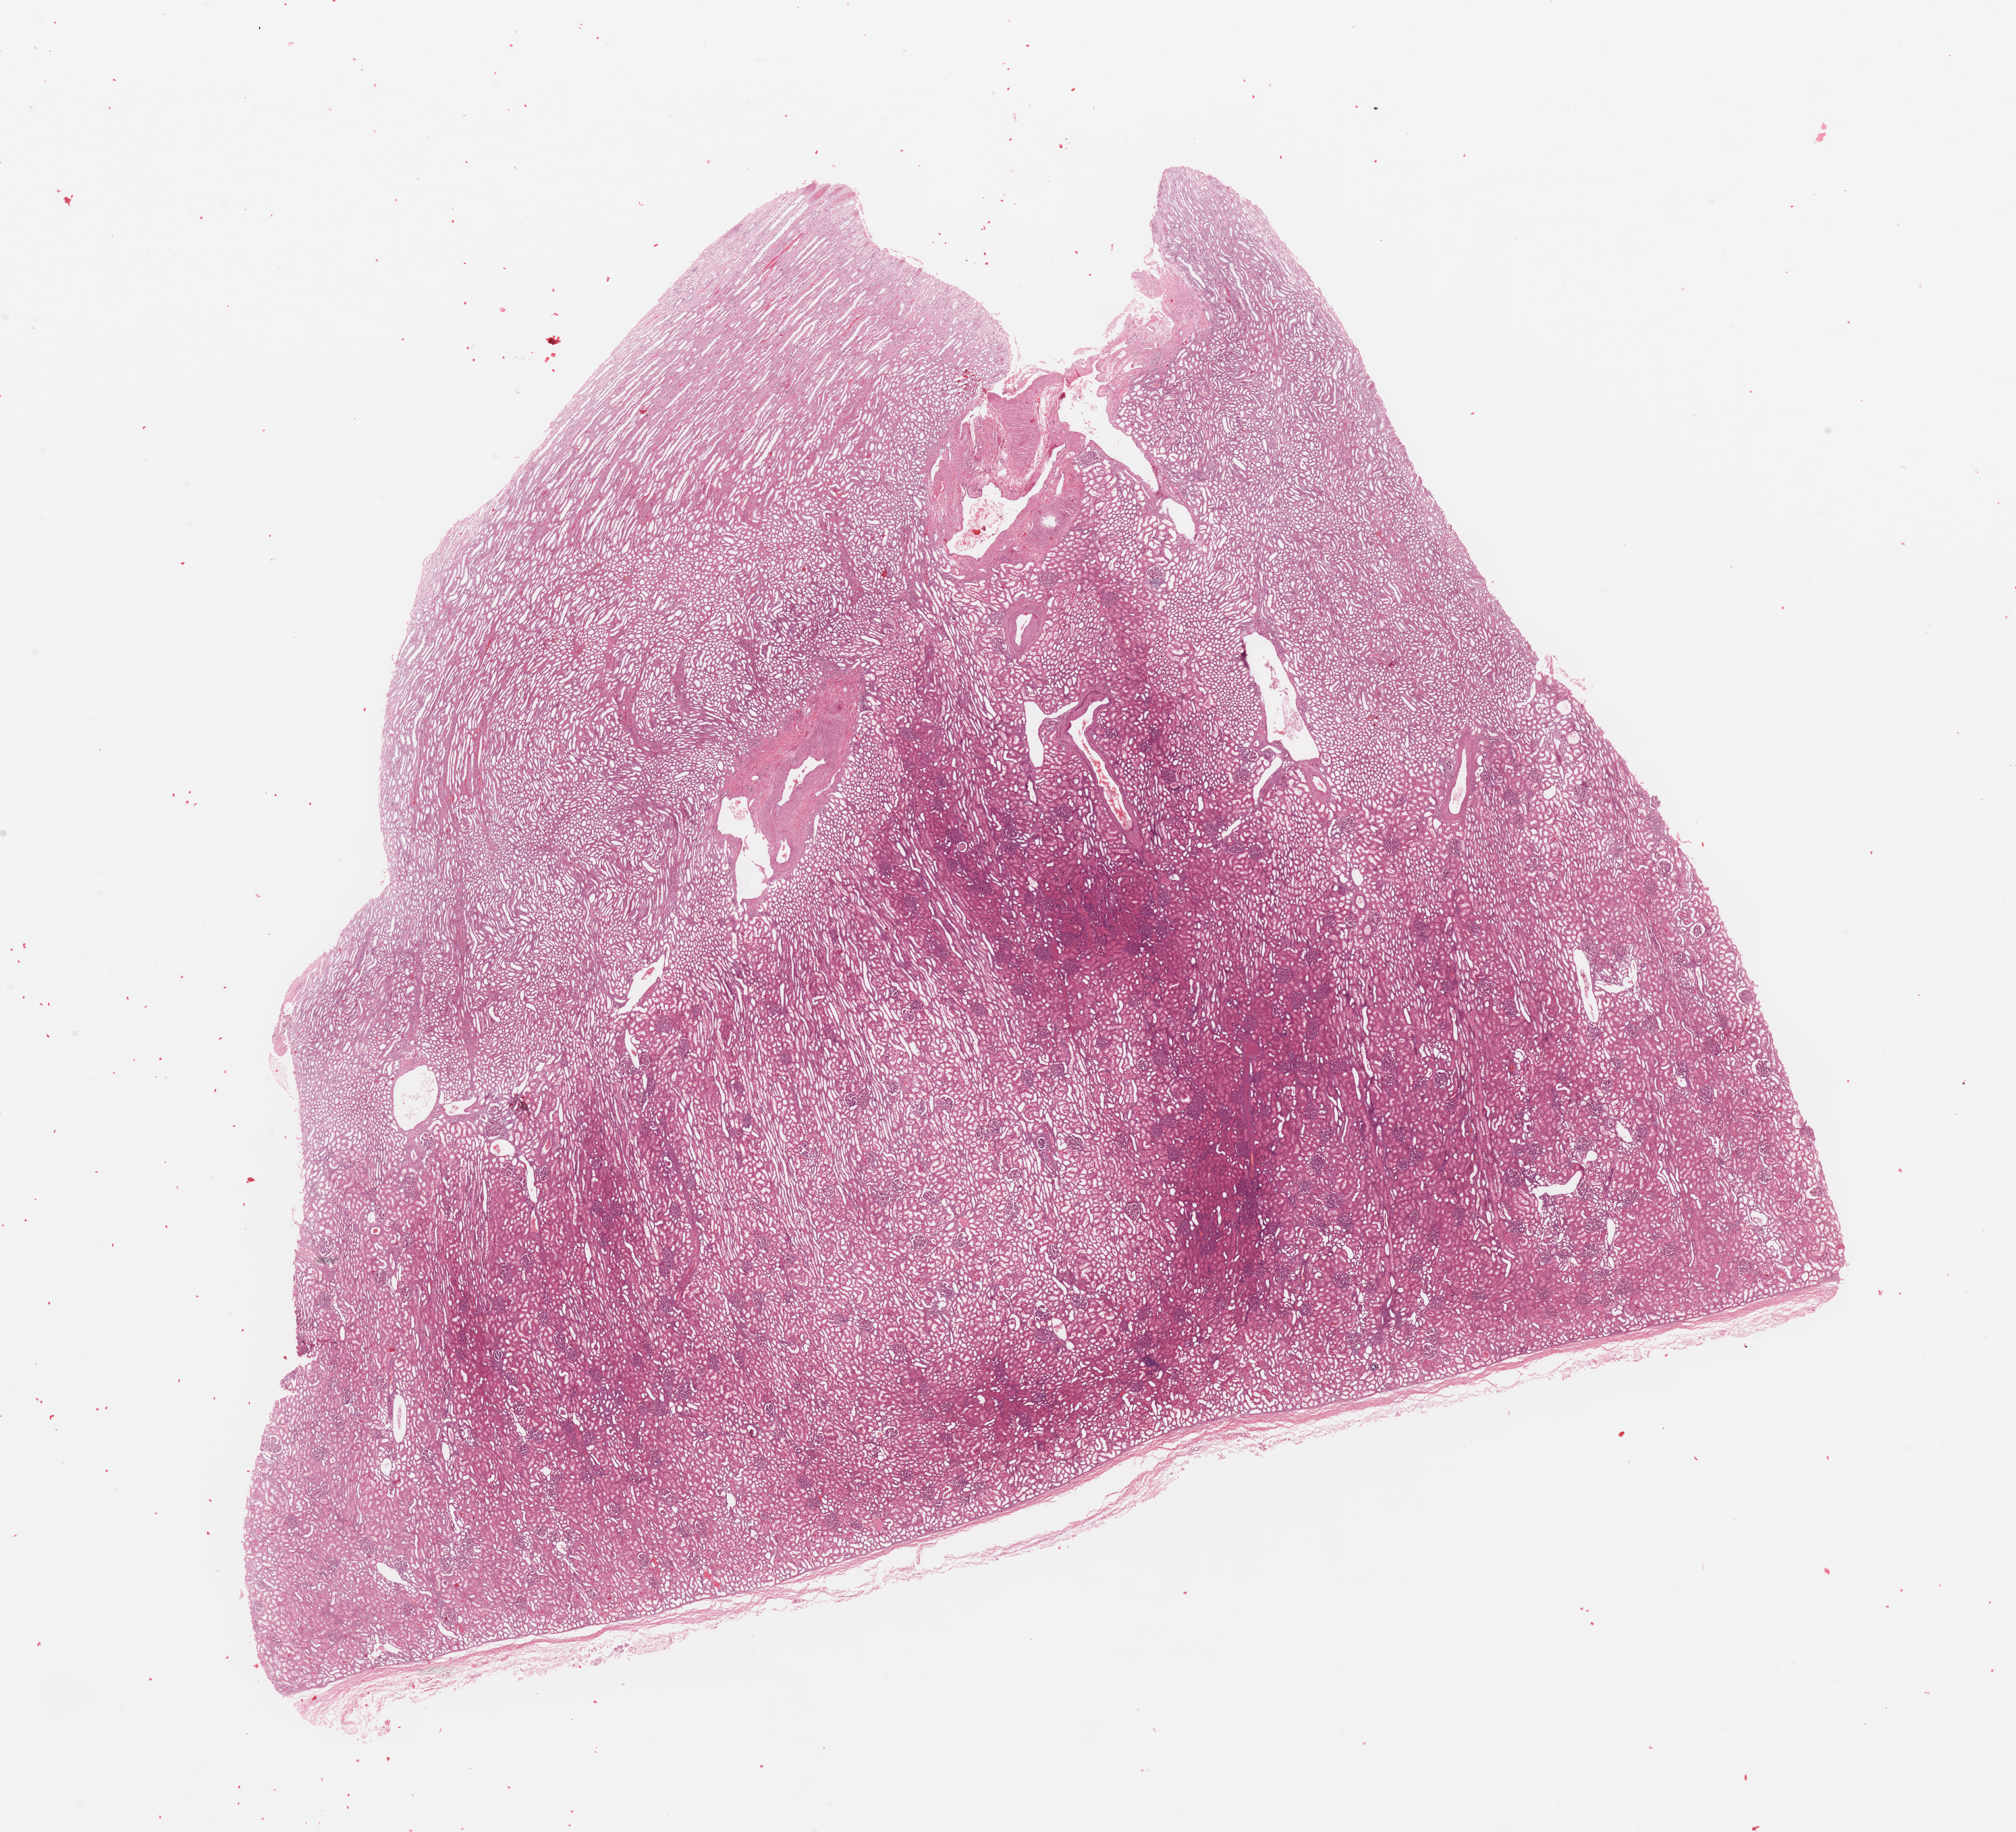
H&E-stained whole-slide image — whole scanned area (about 23.6 x 21.5 mm) shown as a low-resolution overview; normal (non-tumour) tissue sample, sampled site: kidney. 42-year-old female patient.
This section: normal (non-tumour) tissue from the same patient. Patient diagnosis: Renal cell carcinoma, NOS.